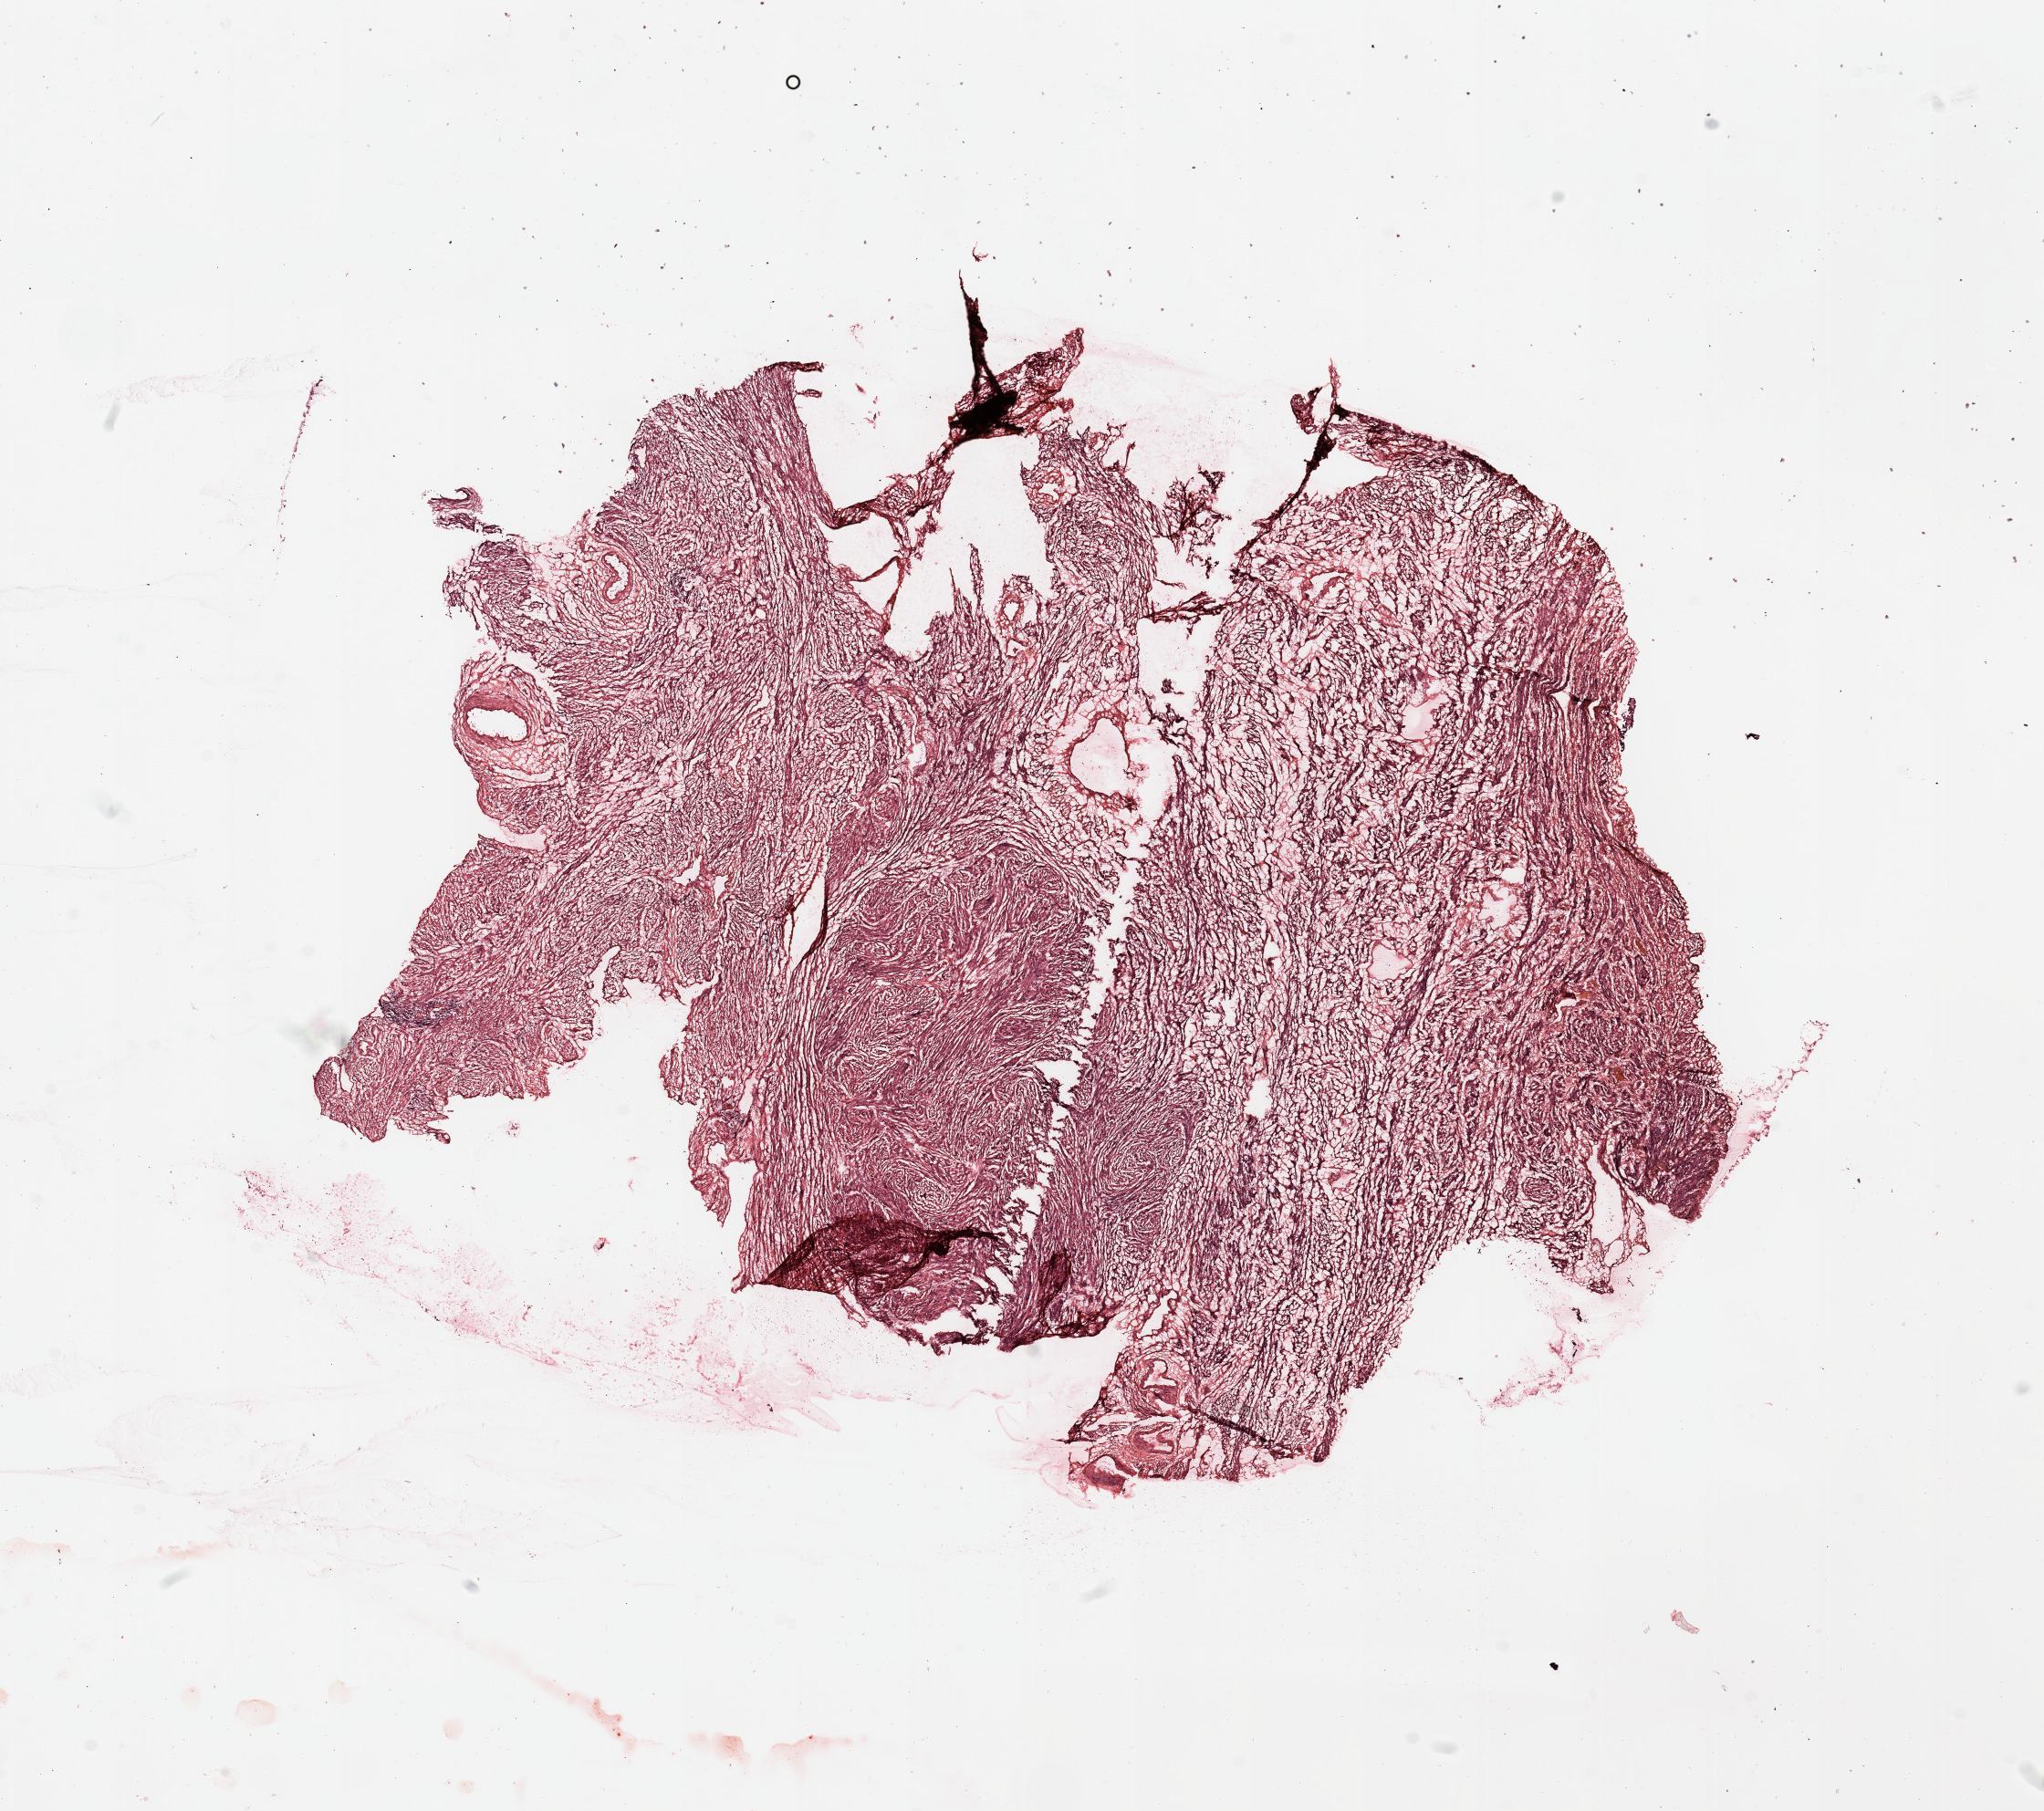
Whole-slide histology image, H&E — low-resolution overview of the scanned area, about 17.7 x 15.7 mm (acquisition: 20x scan), normal (non-tumour) tissue sample, uterus. Female, 57 y/o.
This section: normal (non-tumour) tissue from the same patient. Patient diagnosis: Endometrioid adenocarcinoma, NOS.